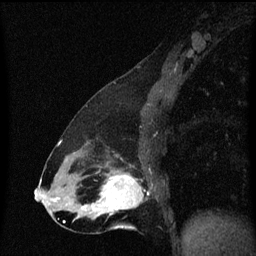
Breast MRI (dynamic contrast-enhanced), one sagittal slice. Slice 30 of 60 in the series (ordered by position). Dynamic contrast-enhanced series, image 2 of 3 at this slice position (ordered by acquisition). 1.5 T. TE 4.2 ms, TR 8.4 ms. 2 mm slice thickness. 256 × 256 image matrix, field of view 200 × 200 mm. Female patient, age 47 years.
Structures marked on this image (semi-automatically segmented with operator editing):
- analysis volume of interest (the breast-tissue region the enhancement analysis was run in; not a lesion): bounding box (x1, y1, x2, y2) in pixels: (100, 172, 145, 217)
- tumour enhancement mask (voxels above the 70 % enhancement threshold inside the analysis volume of interest): (100, 174, 144, 215)